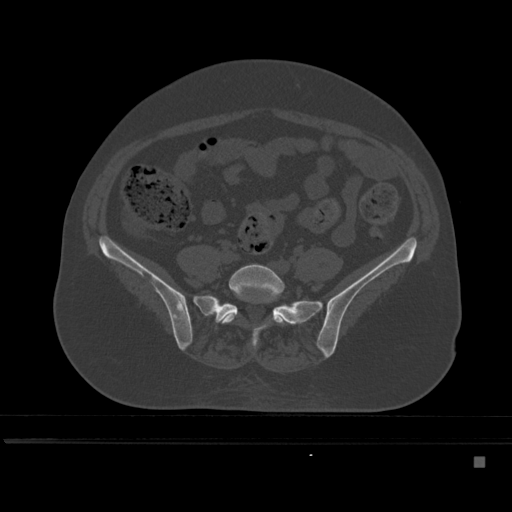
CT including the spine, one axial slice. Slice 101 of 495 in the series (ordered by position). Bone window (W 1800 / L 400 HU). 1.5 mm slice thickness. 512 × 512 image matrix, field of view 404 × 404 mm. Female patient, age 33 years. From the clinical record (not read from this slice): primary cancer: breast; vertebrae with lytic lesions (as recorded): T1.
Structures marked on this image (semi-automatic segmentation, software-assisted and operator-edited):
- L5 vertebra: bounding box <219,263,288,325> (left, top, right, bottom; pixels)